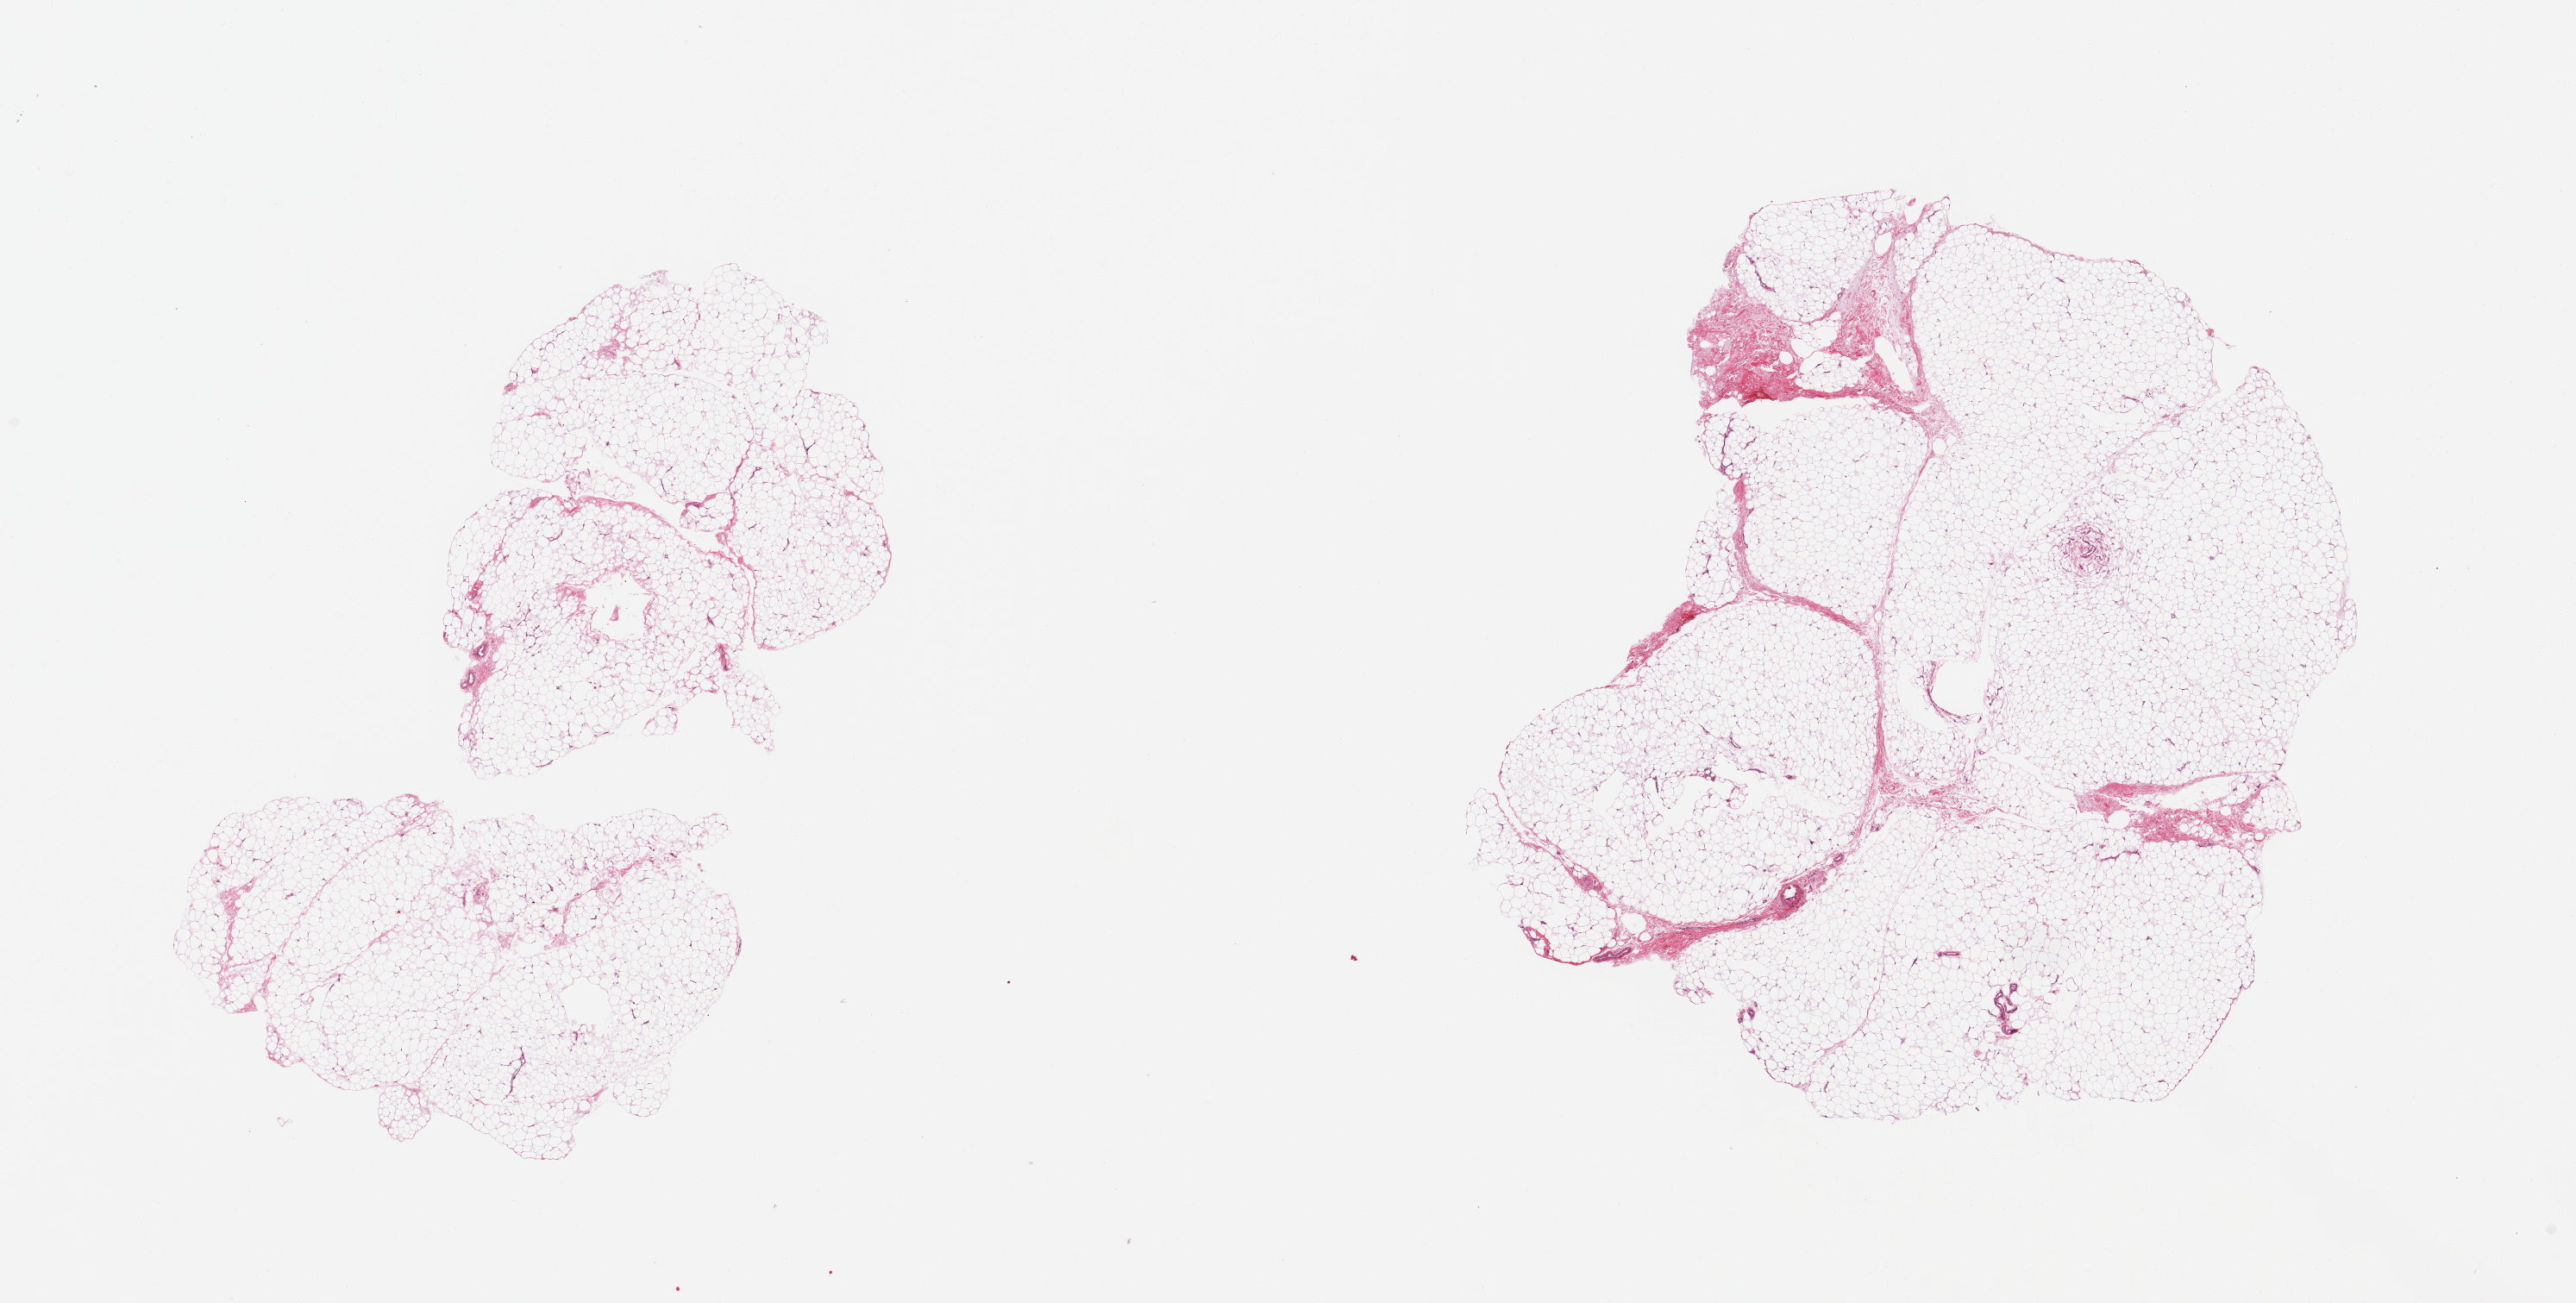
Whole-slide image, H&E stain, brightfield, low-resolution overview of the scanned area, about 23.6 x 12.0 mm (from a 20x scan), PAXgene-fixed, paraffin-embedded tissue, section of adipose tissue (target tissue), tissue donor sample. Male donor.
* reviewer comment on this tissue sample: 2 pieces; mature fat